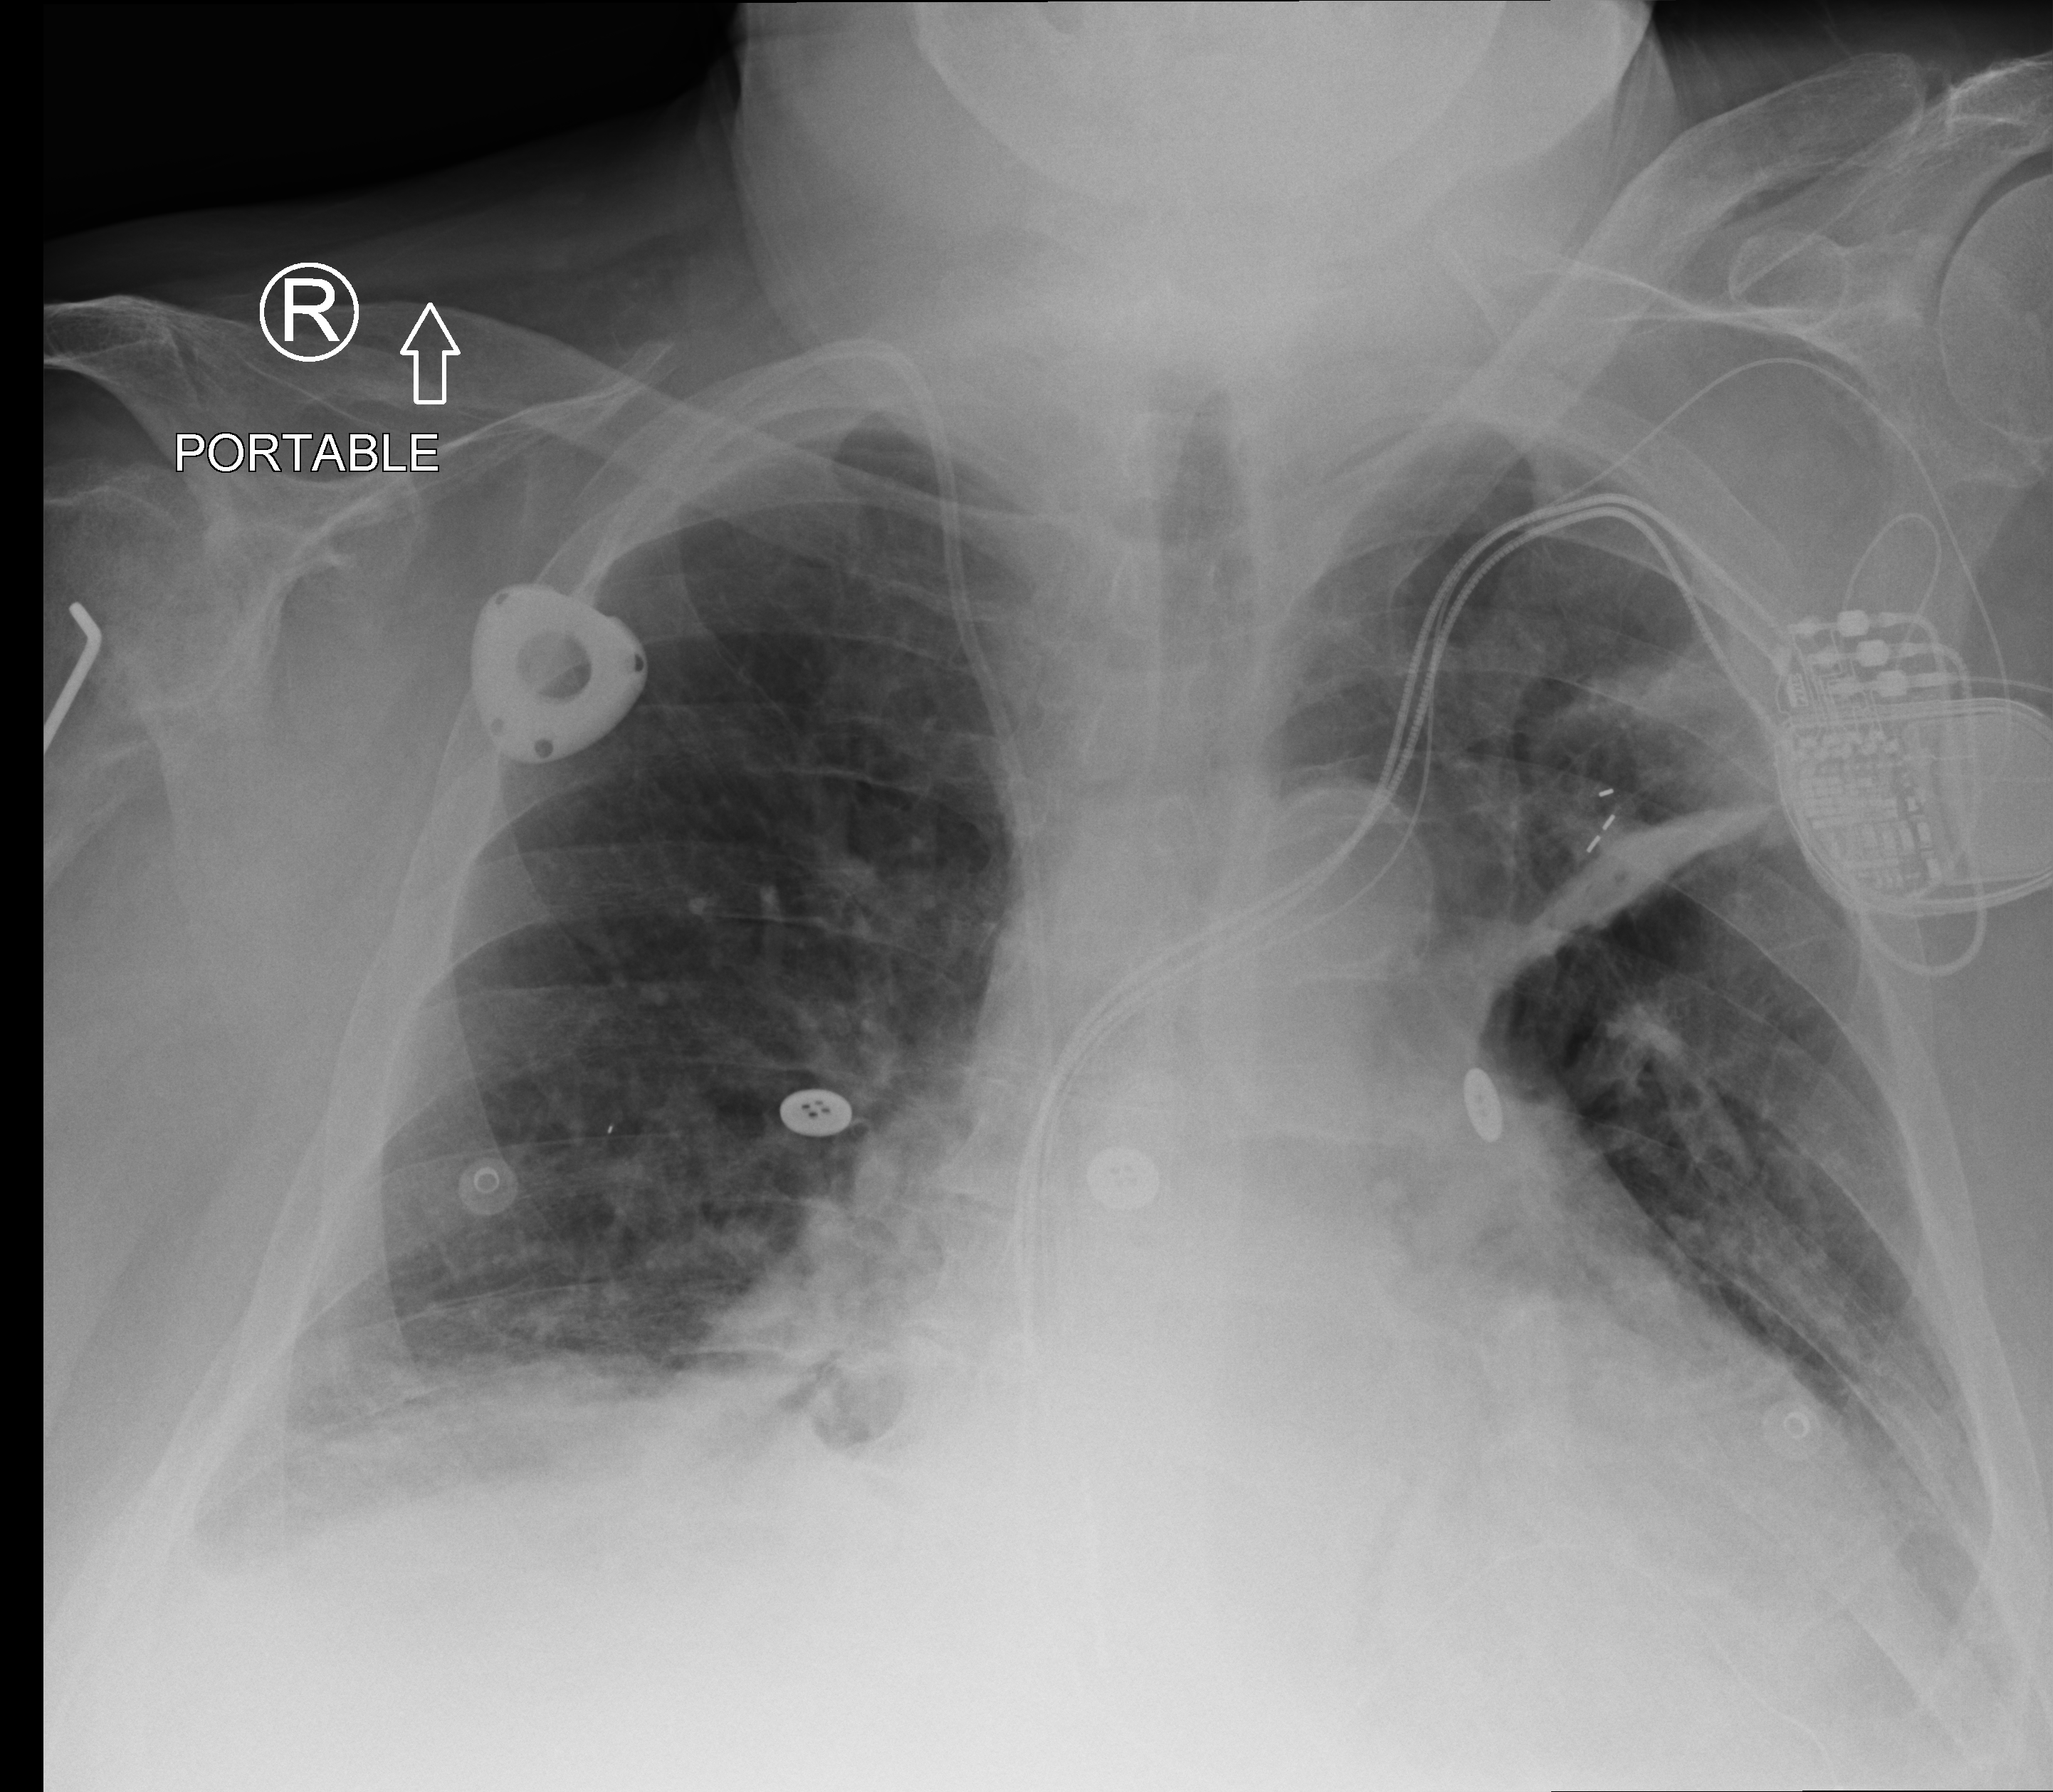
Portable chest radiograph; anteroposterior (AP) projection. Patient hospitalised with COVID-19; male, aged 60–74 years.
Admission-level facts for this patient (not findings on this image; timing relative to this image not recorded):
- admitted to intensive care during this hospital stay: yes
- mechanically ventilated during this hospital stay: no